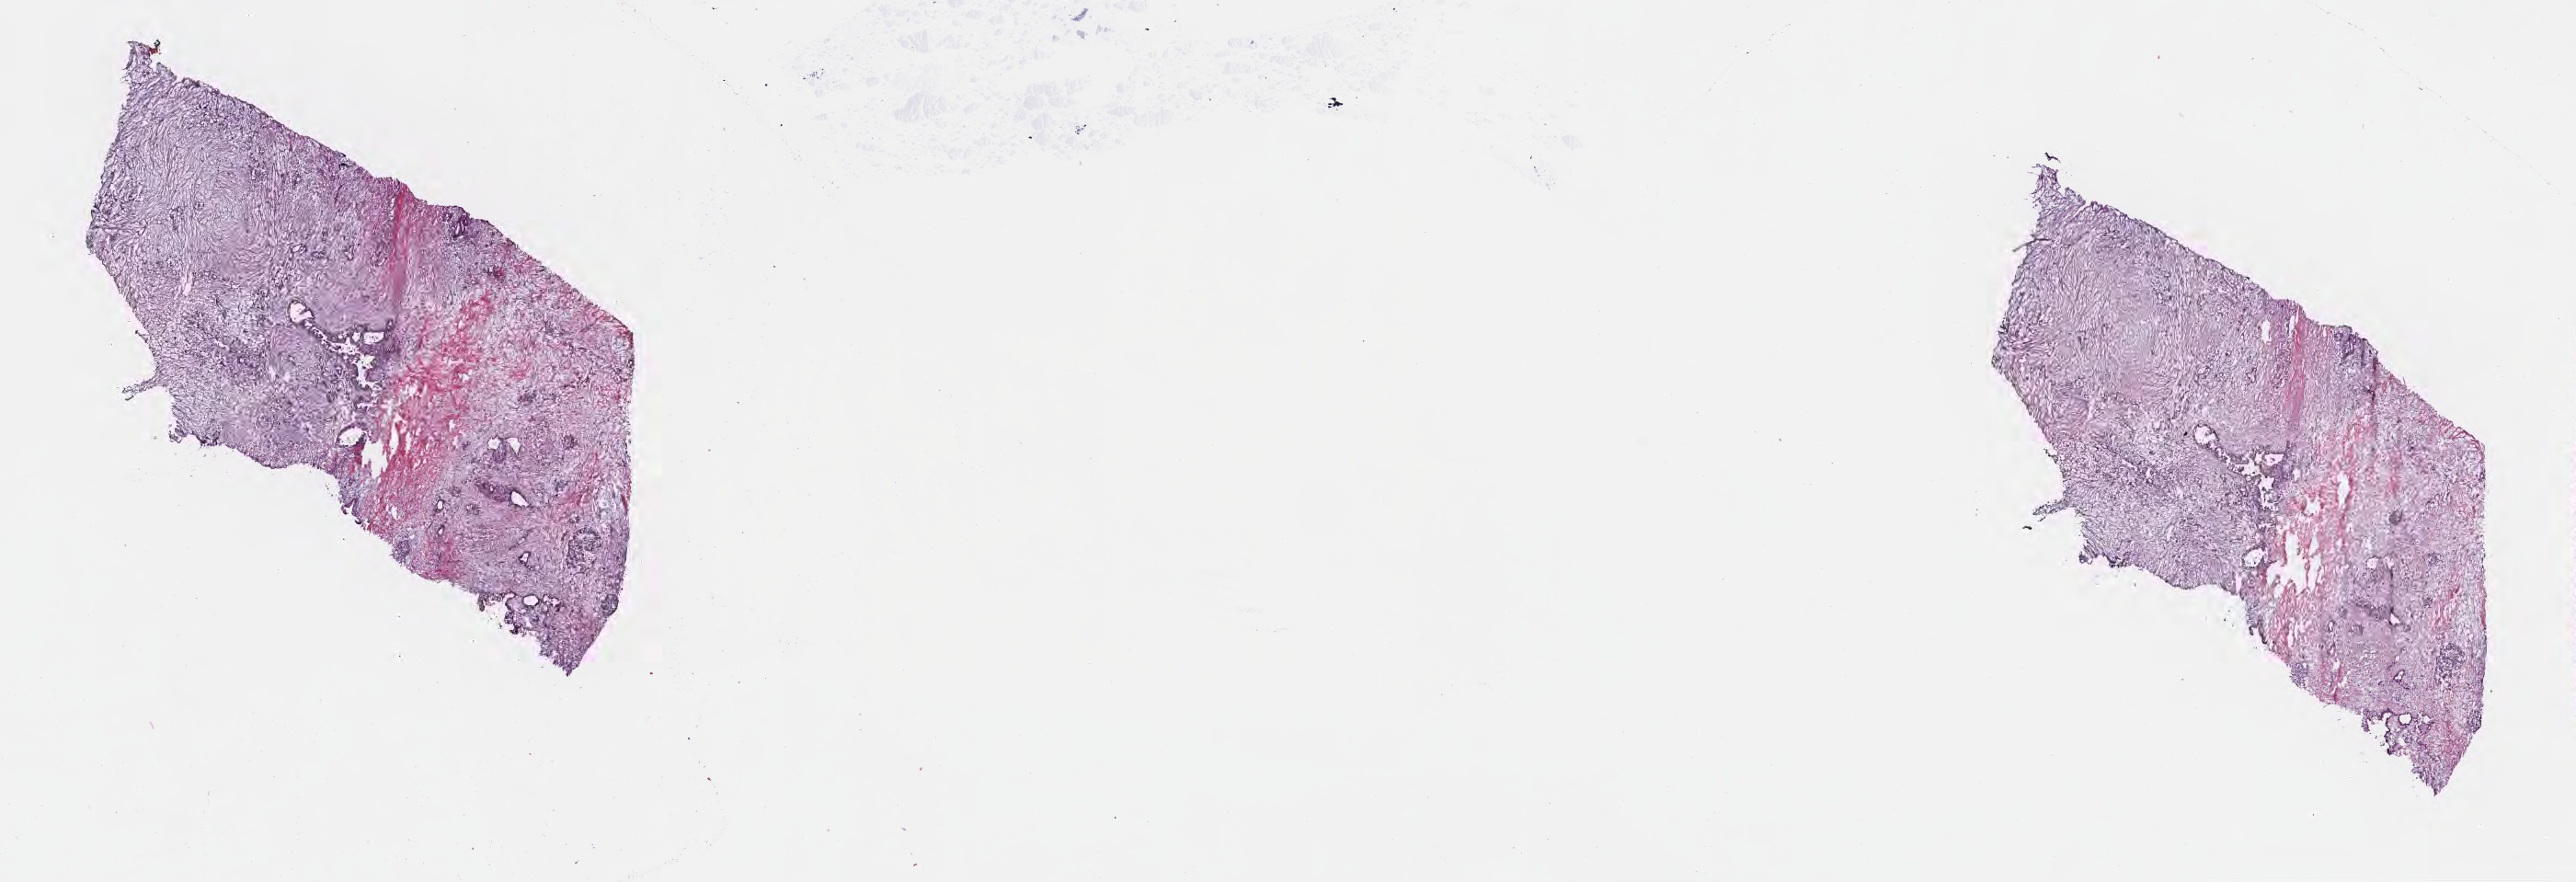
Digitized H&E-stained section, whole scanned area (about 22.7 x 7.8 mm) shown as a low-resolution overview. Frozen section. Specimen: primary tumor. Anatomic site: tail of pancreas. Female patient; age at initial diagnosis 64 years. Tumor grade: G3 (poorly differentiated). Composition of this section per pathologist review: tumor cells 65%, tumor nuclei 65%, stromal cells 30%, necrosis 0%, normal cells 5%. Infiltration values recorded for this section: lymphocyte infiltration 7%, monocyte infiltration 2%, neutrophil infiltration 12%.
* histologic diagnosis: Infiltrating duct carcinoma, NOS
* section: top of the tissue portion
* AJCC pathologic stage: Stage III